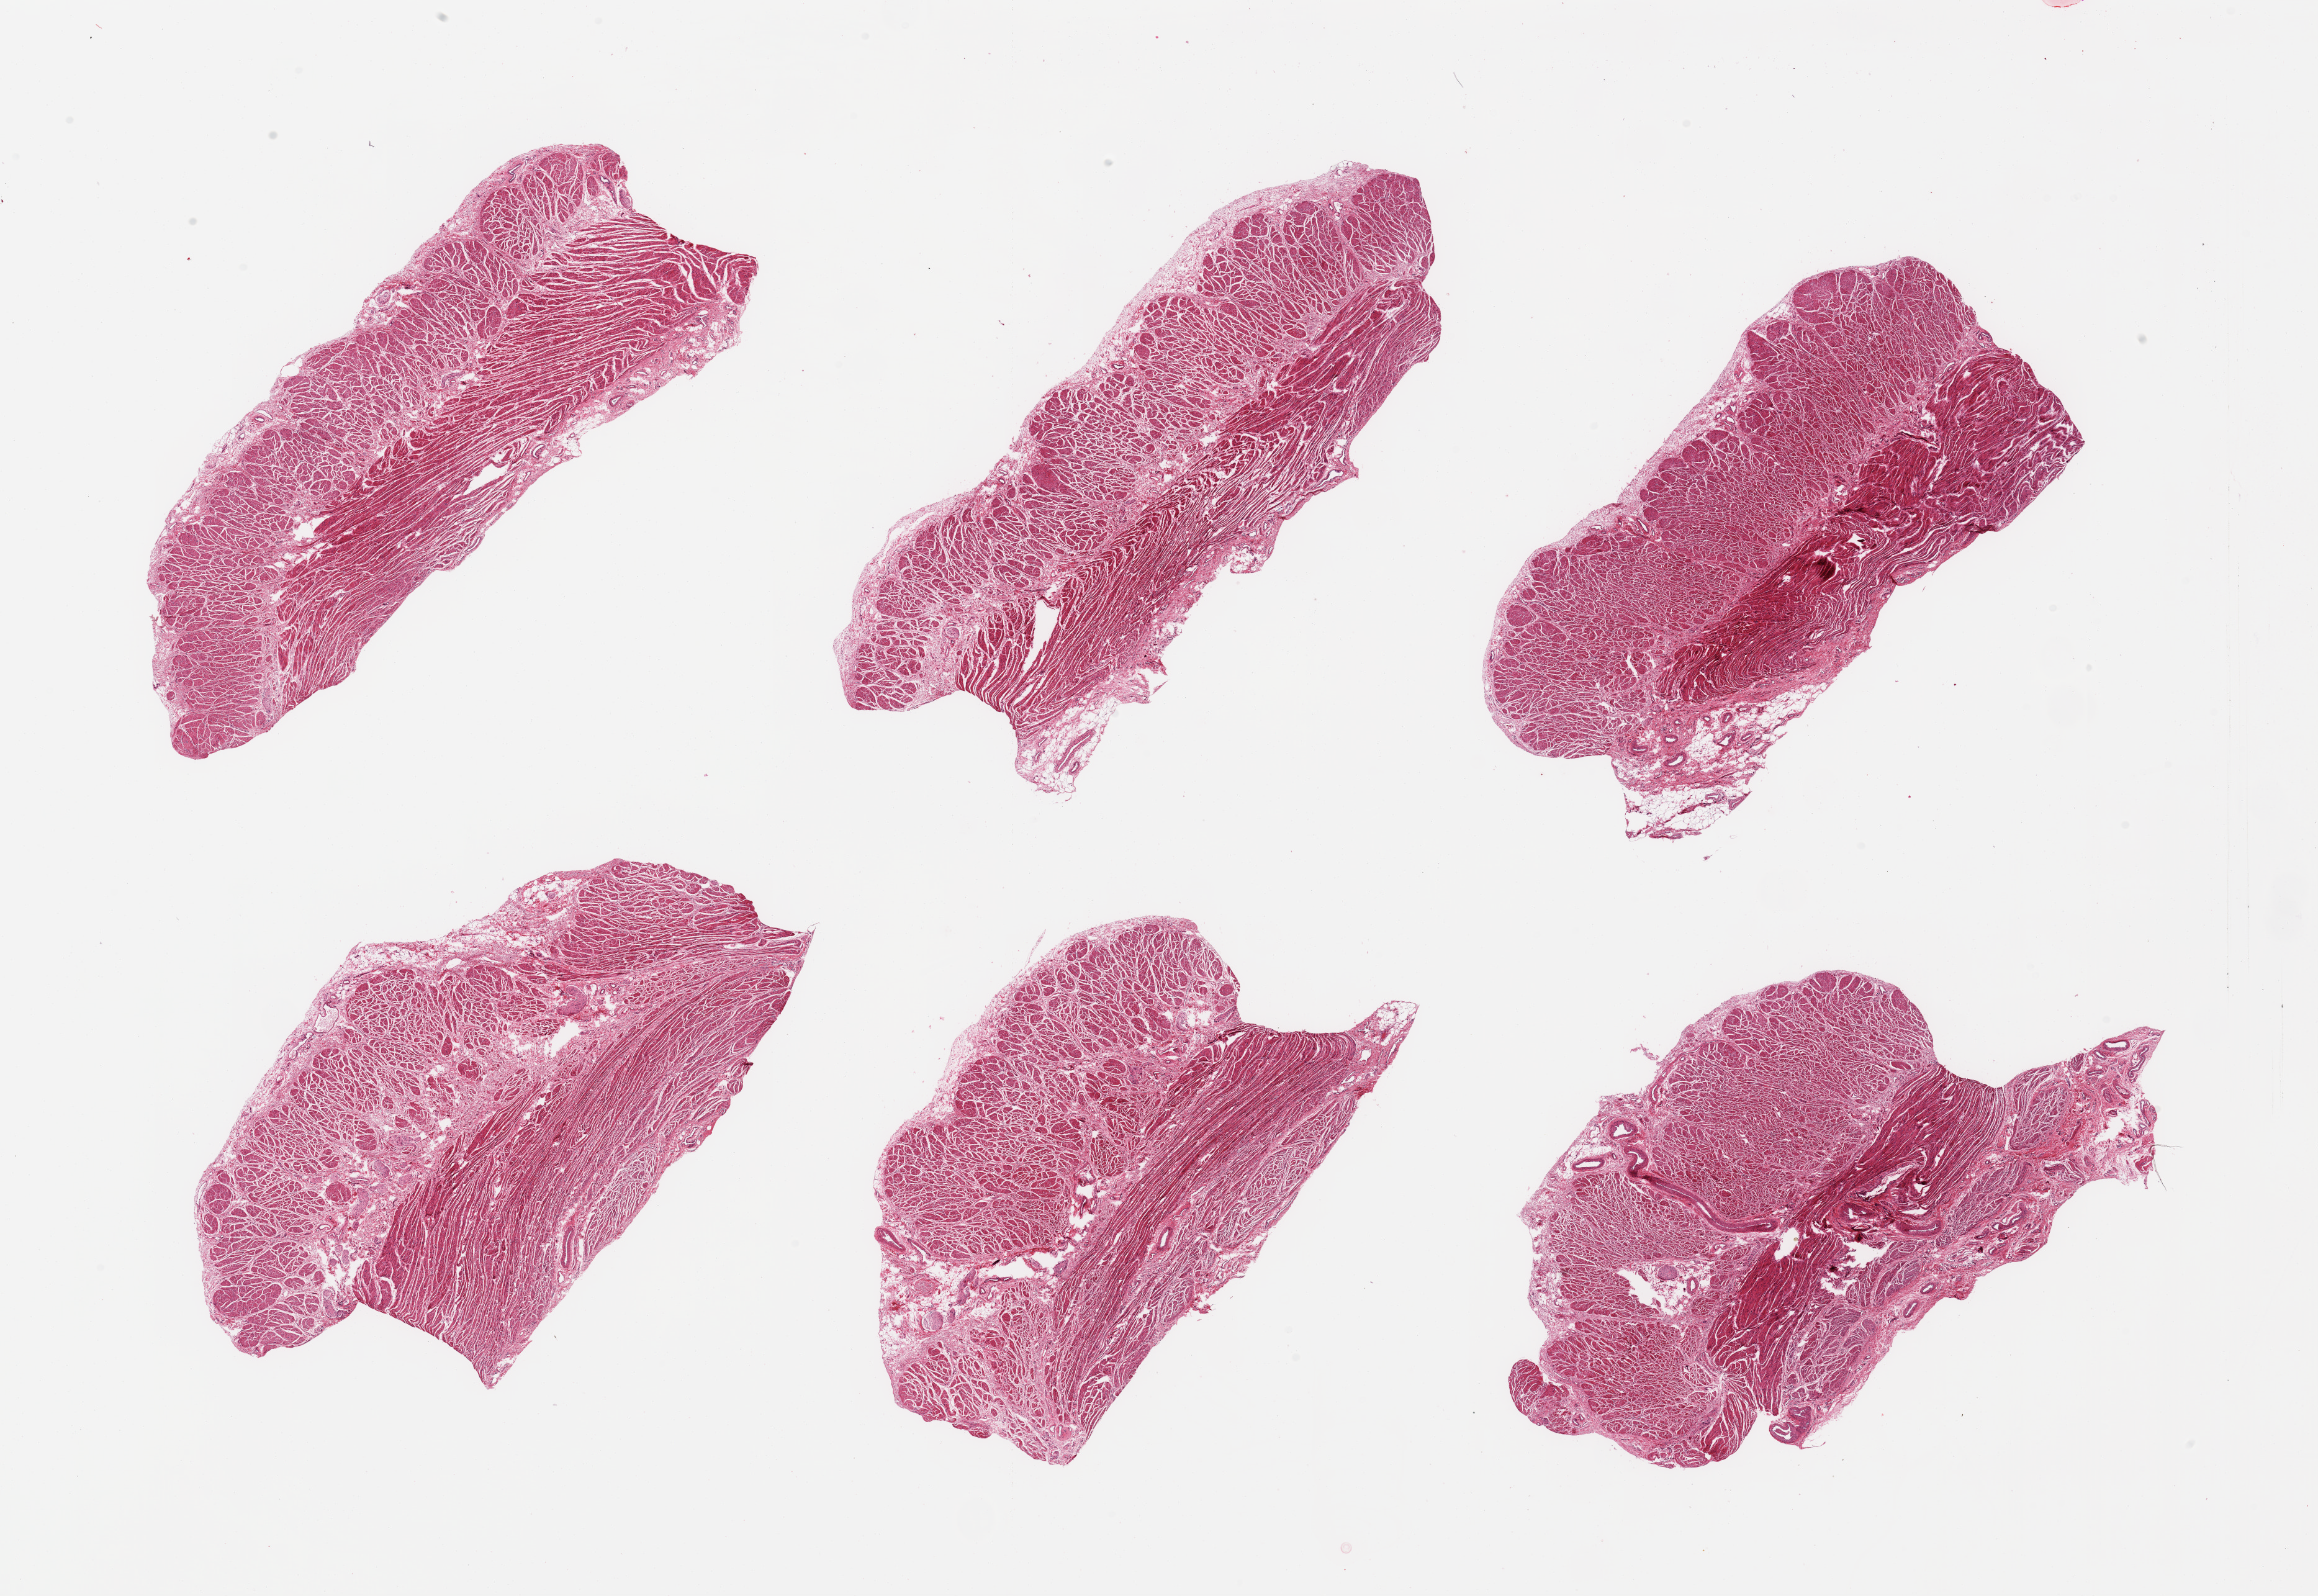
Whole-slide image, haematoxylin and eosin stain — whole scanned area (about 29.5 x 20.3 mm) shown as a low-resolution overview; PAXgene-fixed, paraffin-embedded tissue; target tissue: gastroesophageal junction; tissue donor sample. Male donor.
Pathologist's review note for this sample: 6 pieces, confirmed target muscularis.